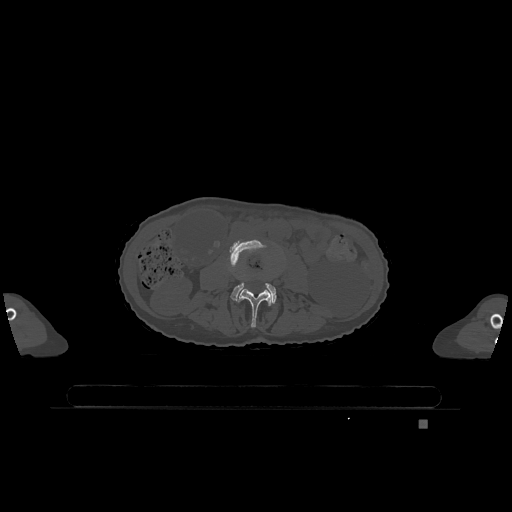
CT including the spine, one axial slice. Slice 336 of 1317 in the series (ordered by position). Bone window (W 1800 / L 400 HU). 512 × 512 image matrix, field of view 500 × 500 mm. Female patient, age 74 years. From the clinical record (not read from this slice): primary cancer: lung; vertebrae with lytic lesions (as recorded): T1, T4, T5, T6, L4, L5.
Annotated regions visible in this slice (semi-automatic segmentation, software-assisted and operator-edited):
- L3 vertebra: bounding box [x1, y1, x2, y2] px = [238, 289, 272, 328]
- L4 vertebra: [230, 240, 277, 303]